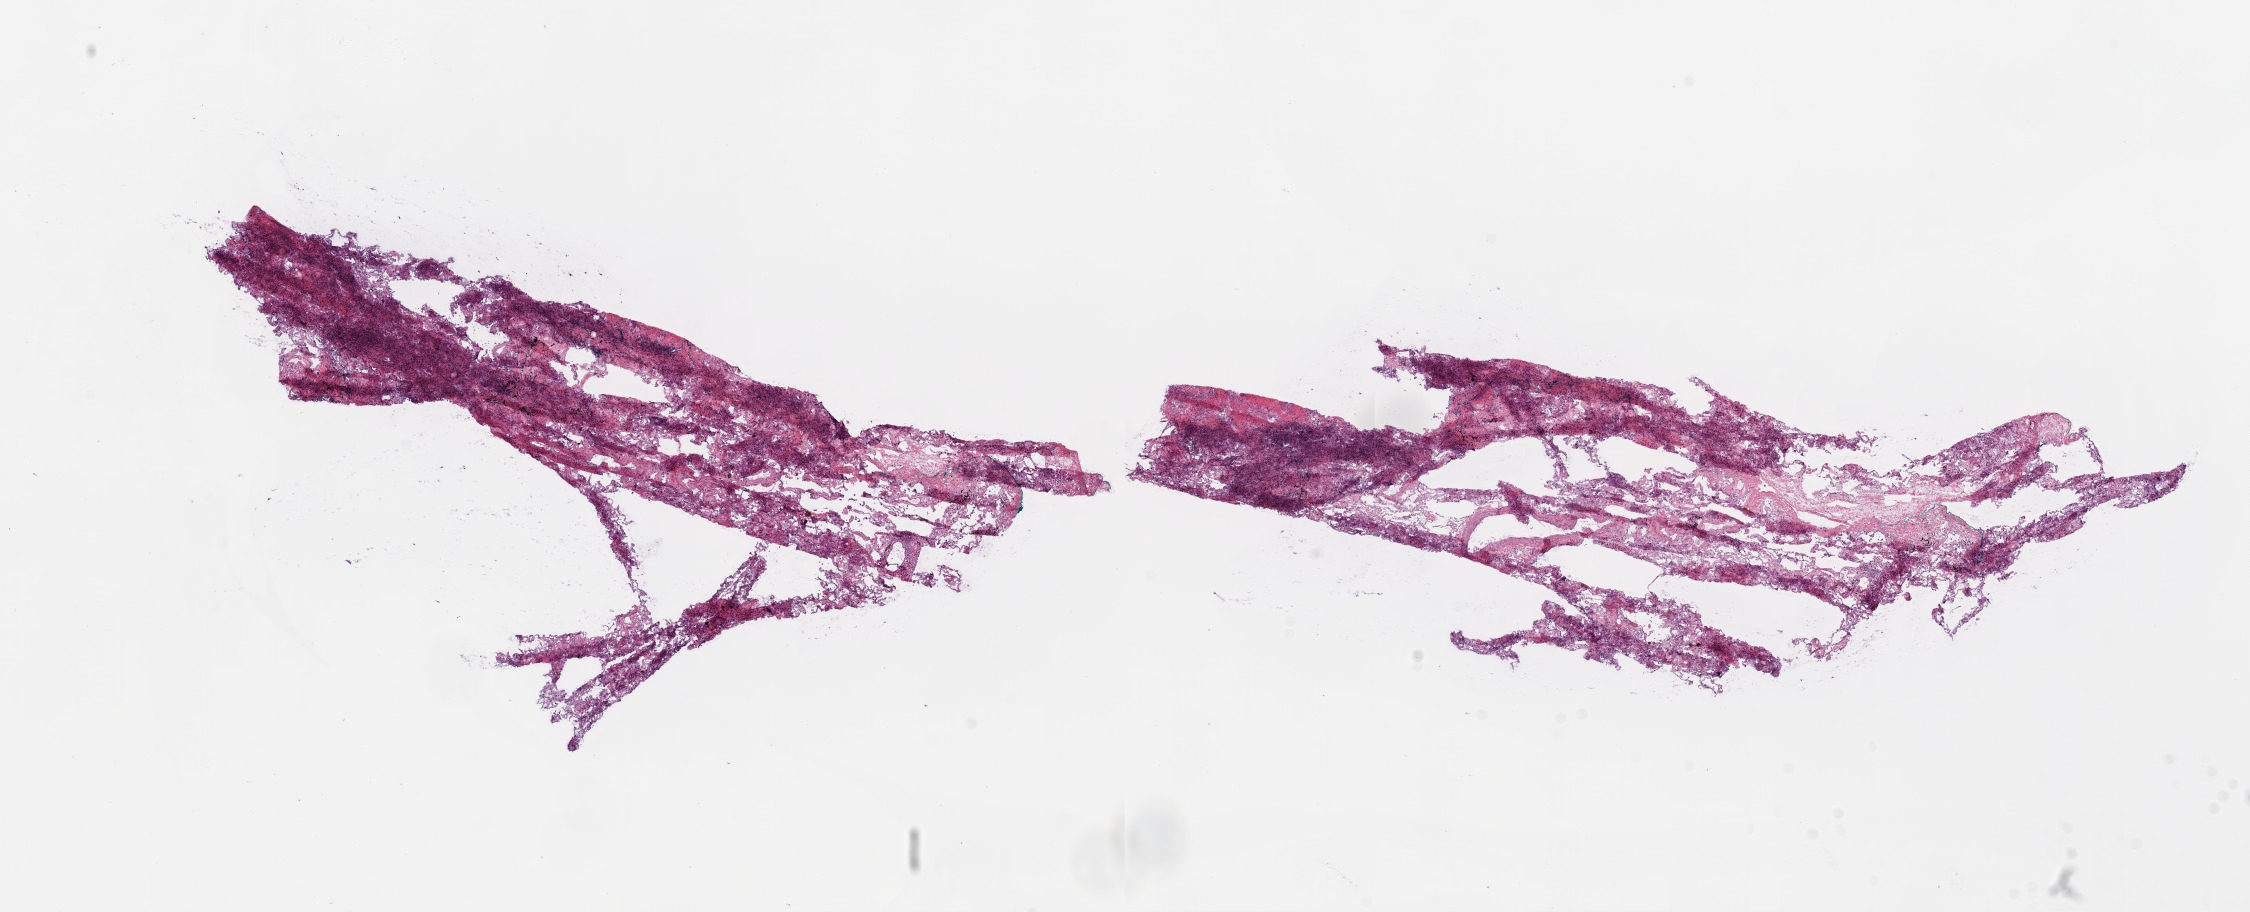
Whole-slide histology image, H&E, whole scanned area (about 18.1 x 7.3 mm, from a 20x scan) shown as a low-resolution overview, frozen section from the bottom of the tissue portion, solid tissue normal (non-tumour tissue) sample from the lung. Female, age 71 years at initial diagnosis.
* this section: solid tissue normal sample (biorepository sample class)
* patient diagnosis: Adenocarcinoma, NOS (upper lobe, lung)